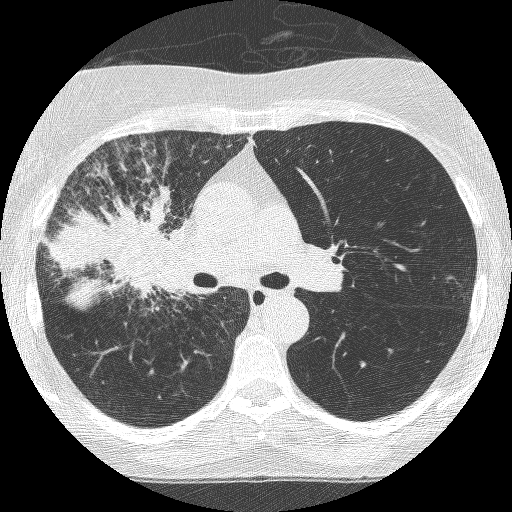
Low-dose screening chest CT, axial slice; third screening round (two years after baseline); lung window (W 1500 / L -600 HU); 1.25 mm slice thickness; lung (sharp) reconstruction kernel (BONE); slice 159 of 253 in the series; 512 × 512 image matrix. Female, age 64 years at enrolment.
Lesion marked by an expert reader, bounding box (x1, y1, x2, y2) in pixels: (77, 199, 203, 326). Screening reader's record for this exam (one nodule recorded; not confirmed to be the boxed lesion): non-calcified nodule or mass ≥4 mm, right upper lobe, 49 × 43 mm, spiculated (stellate) margins, soft tissue attenuation, pre-existing on the prior screen: yes; interval growth: yes. Official screen result: positive, other. Lung cancer was diagnosed 7 days after this screen: adenocarcinoma, NOS, right upper lobe, right middle lobe, right hilum, stage IV (AJCC 6th edition), 85 mm at pathology.